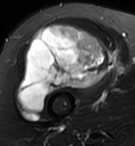
MRI of an extremity soft-tissue mass, one axial slice; position 64 of 95 along the scan axis; T2-weighted fat-saturated; MR volume resampled by the dataset authors to the PET/CT grid (not the native acquisition matrix); 3.27 mm slice thickness; 135 × 146 image matrix. Female patient. From the clinical record (not read from this slice): histological type: pleiomorphic undifferentiated sarcoma; grade: high; site of the primary tumour: right quadricep.
Structures marked on this image (expert contour drawn on MRI and transferred to this co-registered scan by the dataset authors):
- gross tumour volume including surrounding oedema: bounding box <18,24,109,112> (left, top, right, bottom; pixels)
- gross tumour volume (mass): <18,24,109,112>